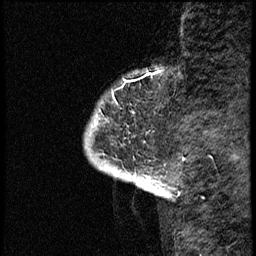
Breast MRI (dynamic contrast-enhanced), one sagittal slice; position 4 of 68 along the scan axis; dynamic contrast-enhanced study with each time point stored as its own series, time point 2 of 3 at this slice position (early post-contrast, ordered by acquisition time); 1.5 T; TE 4.2 ms, TR 17.6 ms; 2 mm slice thickness; 256 × 256 image matrix, field of view 200 × 200 mm. Patient: female, 52 years. From the clinical record (not read from this slice): setting: breast cancer imaged before/during neoadjuvant chemotherapy; receptor status: HER2-positive.
Structures marked on this image (semi-automatic segmentation, software-assisted and operator-edited):
- analysis volume of interest (the breast-tissue region the enhancement analysis was run in; not a lesion): bounding box (x1, y1, x2, y2) in pixels: (85, 66, 176, 184)
- tumour enhancement mask (voxels above the 100 % enhancement threshold inside the analysis volume of interest): (129, 71, 161, 184)